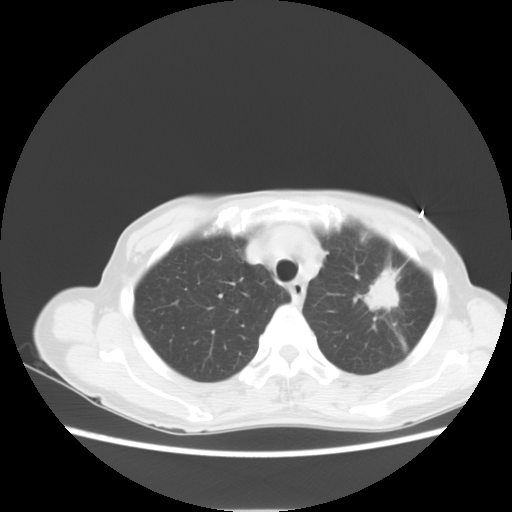
Chest CT, one axial slice. Slice 9 of 14 in the series (ordered by position). Lung window (W 1500 / L -600 HU). 5 mm slice thickness. 512 × 512 image matrix. Female patient, age 71 years. Case-level facts recorded for this patient, not image findings: clinical TNM (as recorded): T2 N0 M0.
Outlined on this slice (rectangle marked by the reading radiologist):
- lung tumour (recorded histology: adenocarcinoma): bounding box [x1, y1, x2, y2] px = [361, 265, 403, 315]